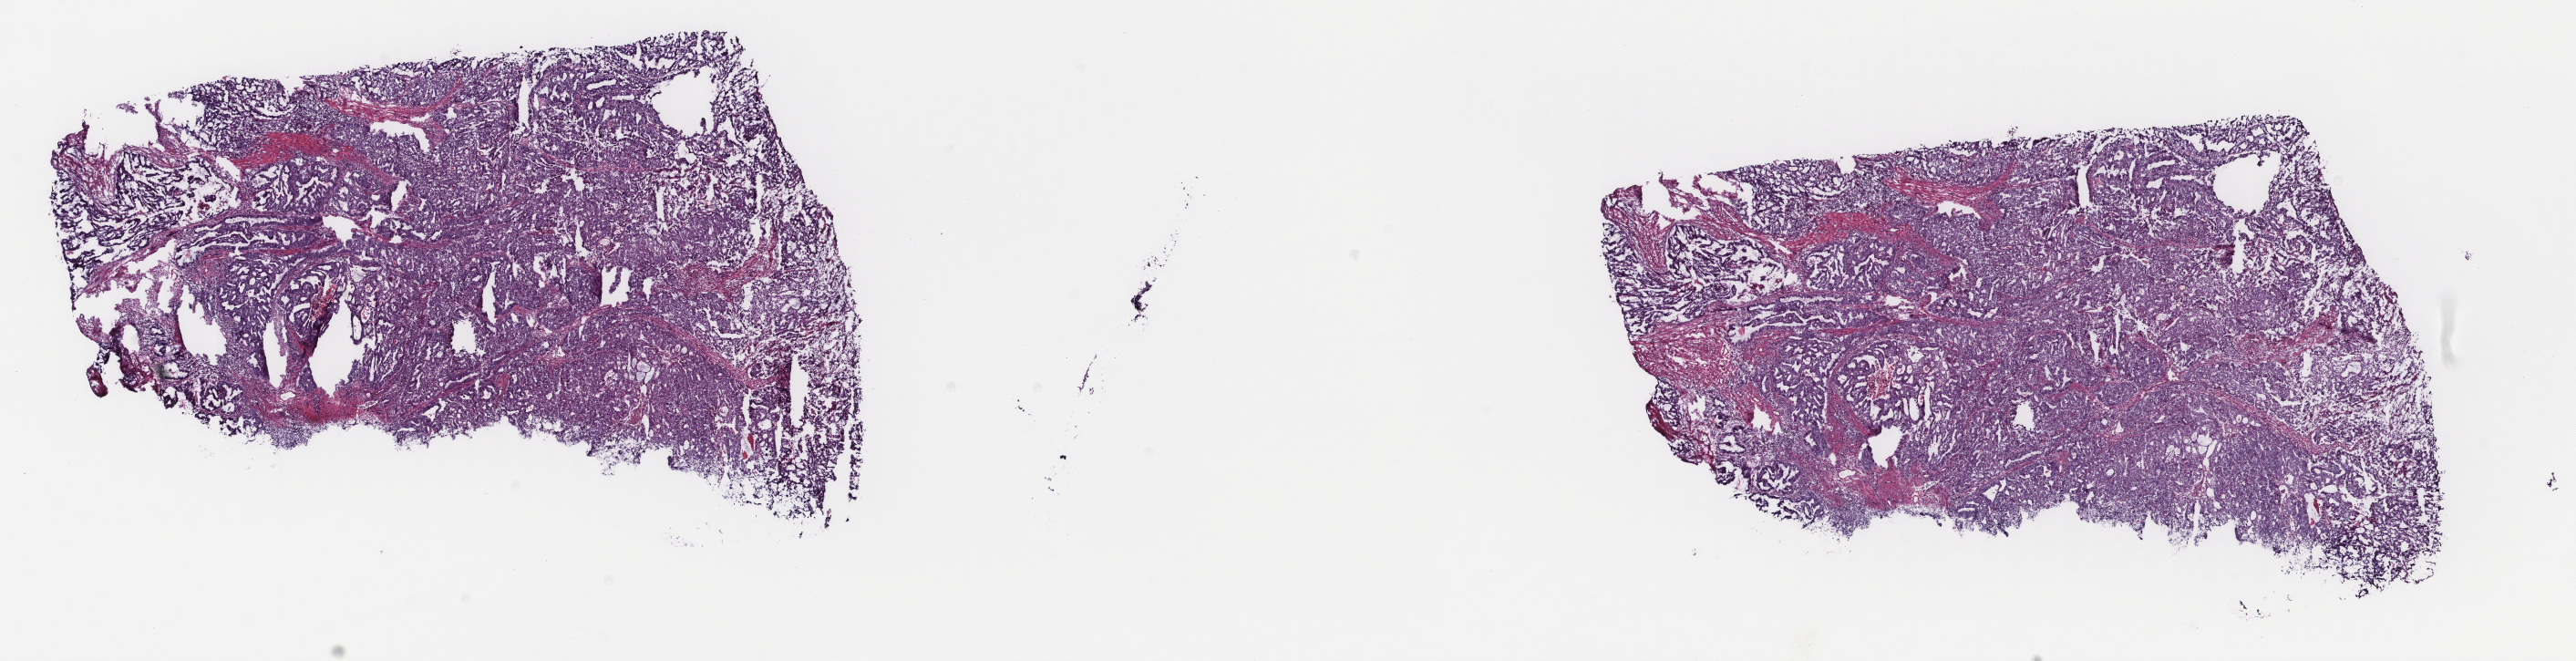
H&E whole-slide image, a low-resolution overview of the entire scanned area, about 22.4 x 5.8 mm, frozen section from the top of the tissue portion, sample: primary tumour, uterus. Patient: female, age at initial diagnosis 70 years. Histologic grade: G2 (moderately differentiated). Composition of this section per pathologist review: tumour cells 95%, tumour nuclei 85%, normal cells 0%, stromal cells 5%, necrosis 0%. Inflammatory infiltration, as recorded: lymphocyte infiltration 0%, monocyte infiltration 0%, neutrophil infiltration 0%.
FIGO stage: IB. Histologic diagnosis: Endometrioid adenocarcinoma, NOS (endometrium).